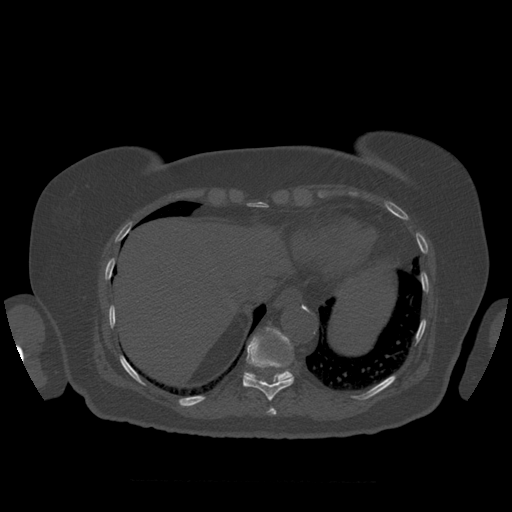
CT including the spine, one axial slice; position 336 of 399 along the scan axis; reconstruction kernel STANDARD; 120 kVp; bone window (W 1800 / L 400 HU); 1.25 mm slice thickness; 512 × 512 image matrix, field of view 404 × 404 mm. Patient age 81 years. From the clinical record (not read from this slice): primary cancer: renal.
Structures marked on this image (semi-automatically segmented with operator editing):
- T10 vertebra: bounding box (x1, y1, x2, y2) in pixels: (243, 336, 295, 401)
- T11 vertebra: (244, 328, 293, 381)
- T9 vertebra: (268, 408, 277, 416)